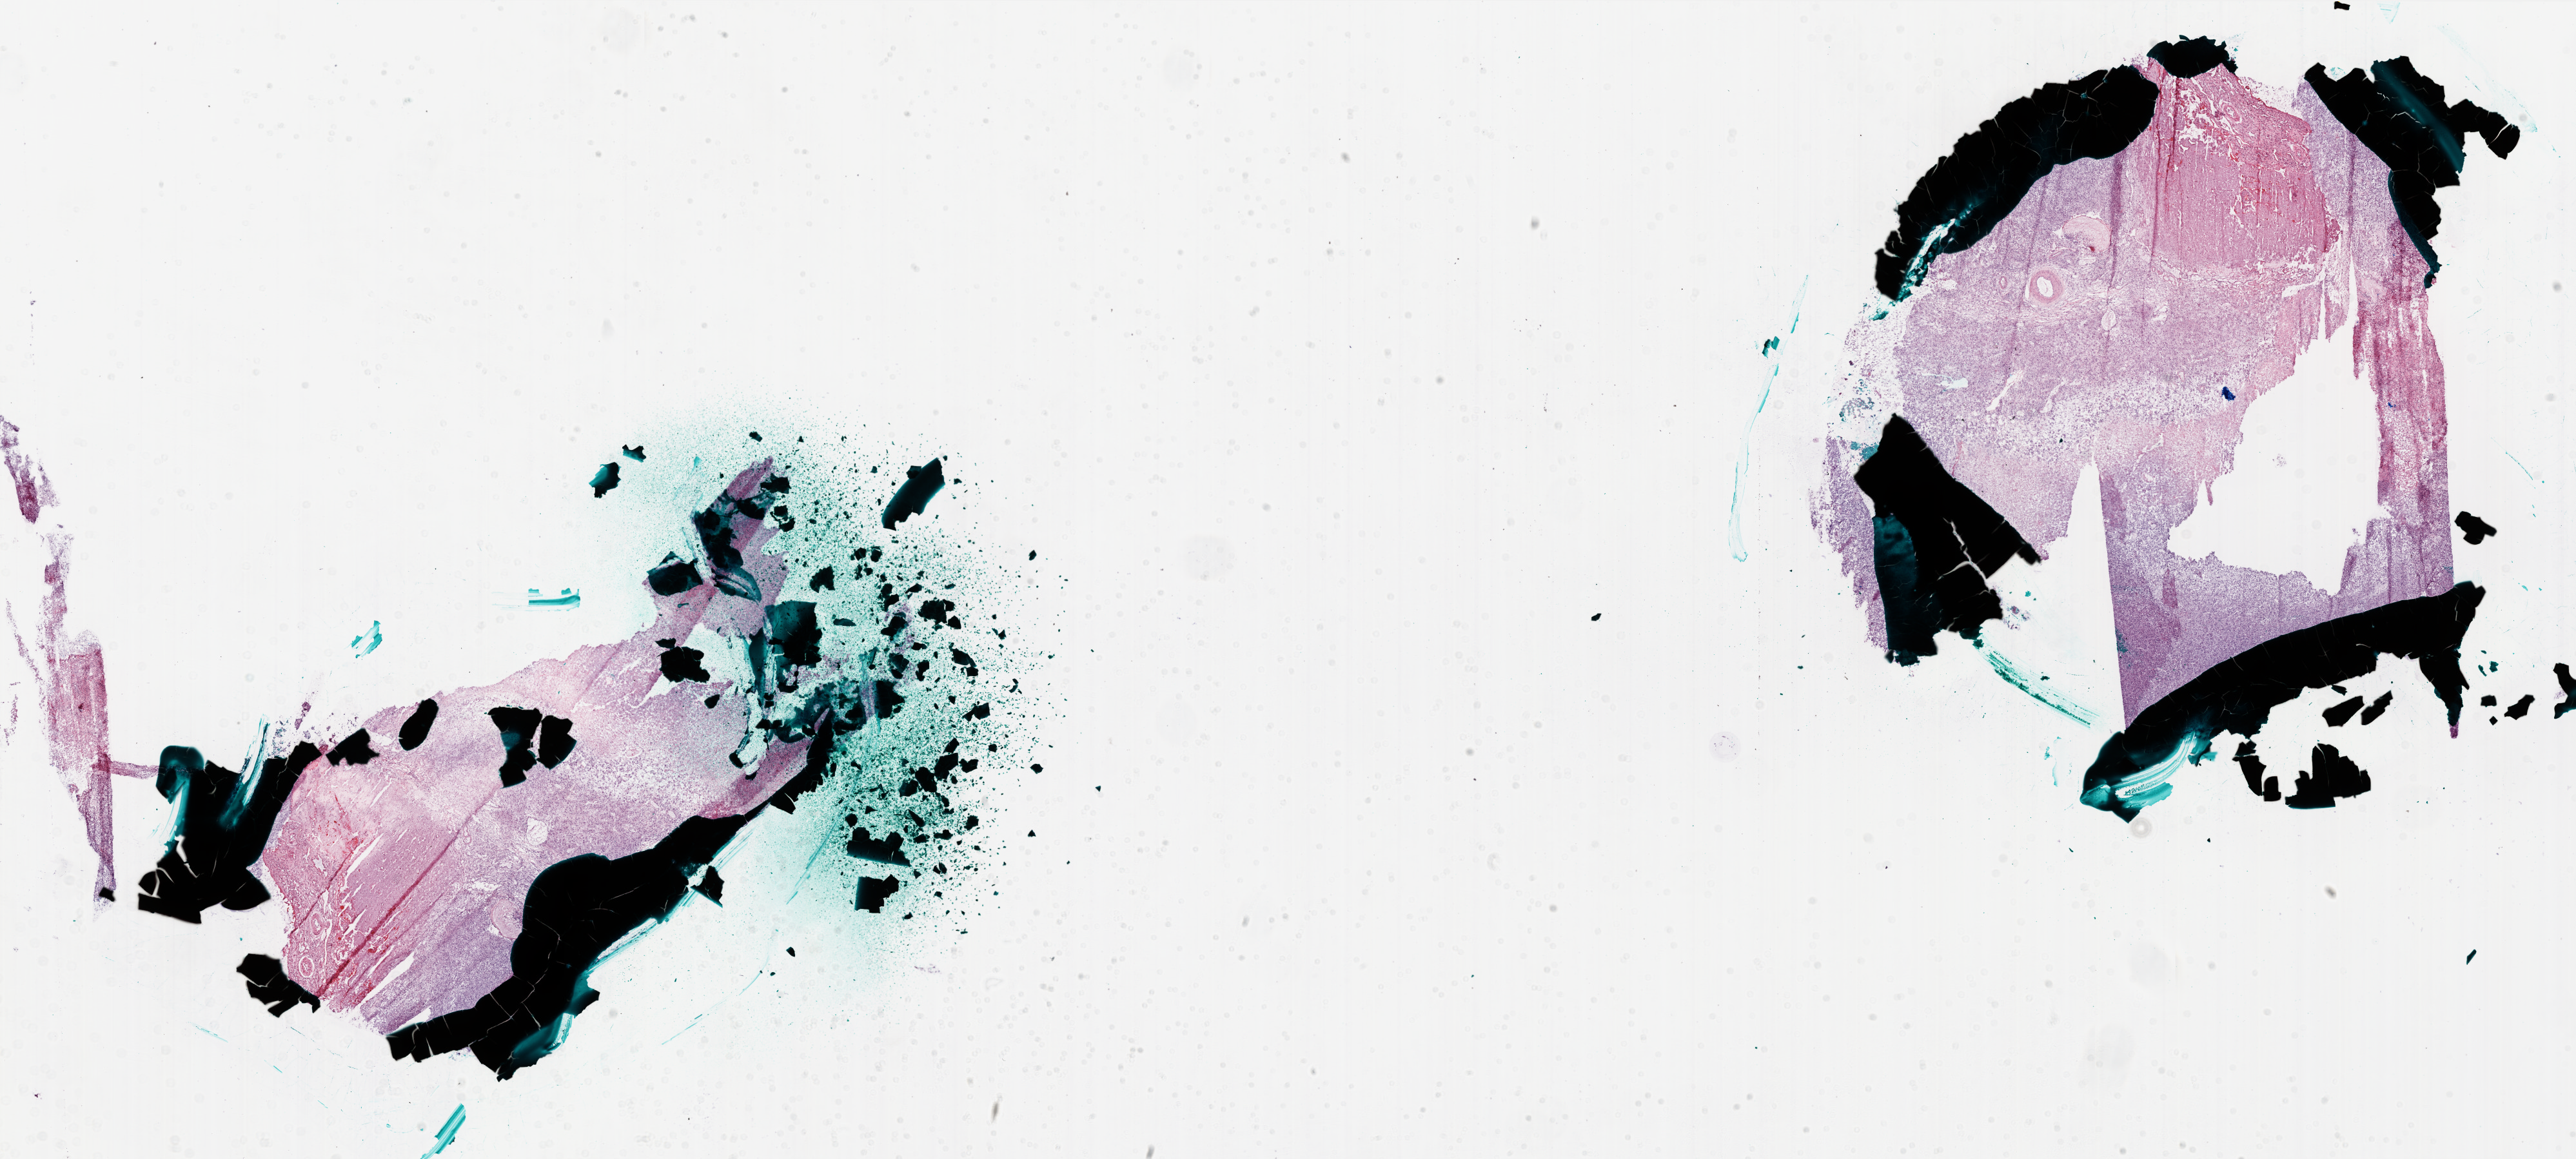
H&E whole-slide image, a low-resolution overview of the entire scanned area, about 32.0 x 14.4 mm (from a 20x scan), frozen section, sample: primary tumour, brain. Male patient; age at initial diagnosis 54 years. Slide review estimates, as recorded: tumour cells 60%, tumour nuclei 90%, normal cells 0%, stromal cells 20%, necrosis 20%.
Diagnosis: Glioblastoma.